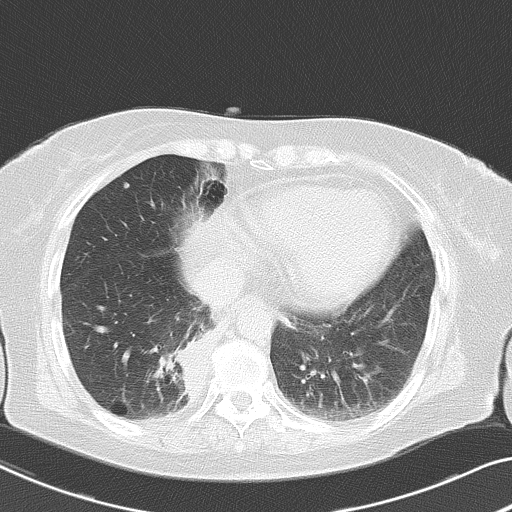
Chest CT, one axial slice. Position 16 of 53 along the scan axis. Reconstruction kernel B70f. Lung window (W 1500 / L -600 HU). 5 mm slice thickness. 512 × 512 image matrix. Female patient, age 70 years. From the clinical record (not read from this slice): clinical TNM (as recorded): T2 N1 M1a.
Structures marked on this image (rectangle marked by the reading radiologist):
- lung tumour (recorded histology: adenocarcinoma): bounding box <164,320,212,400> (left, top, right, bottom; pixels)